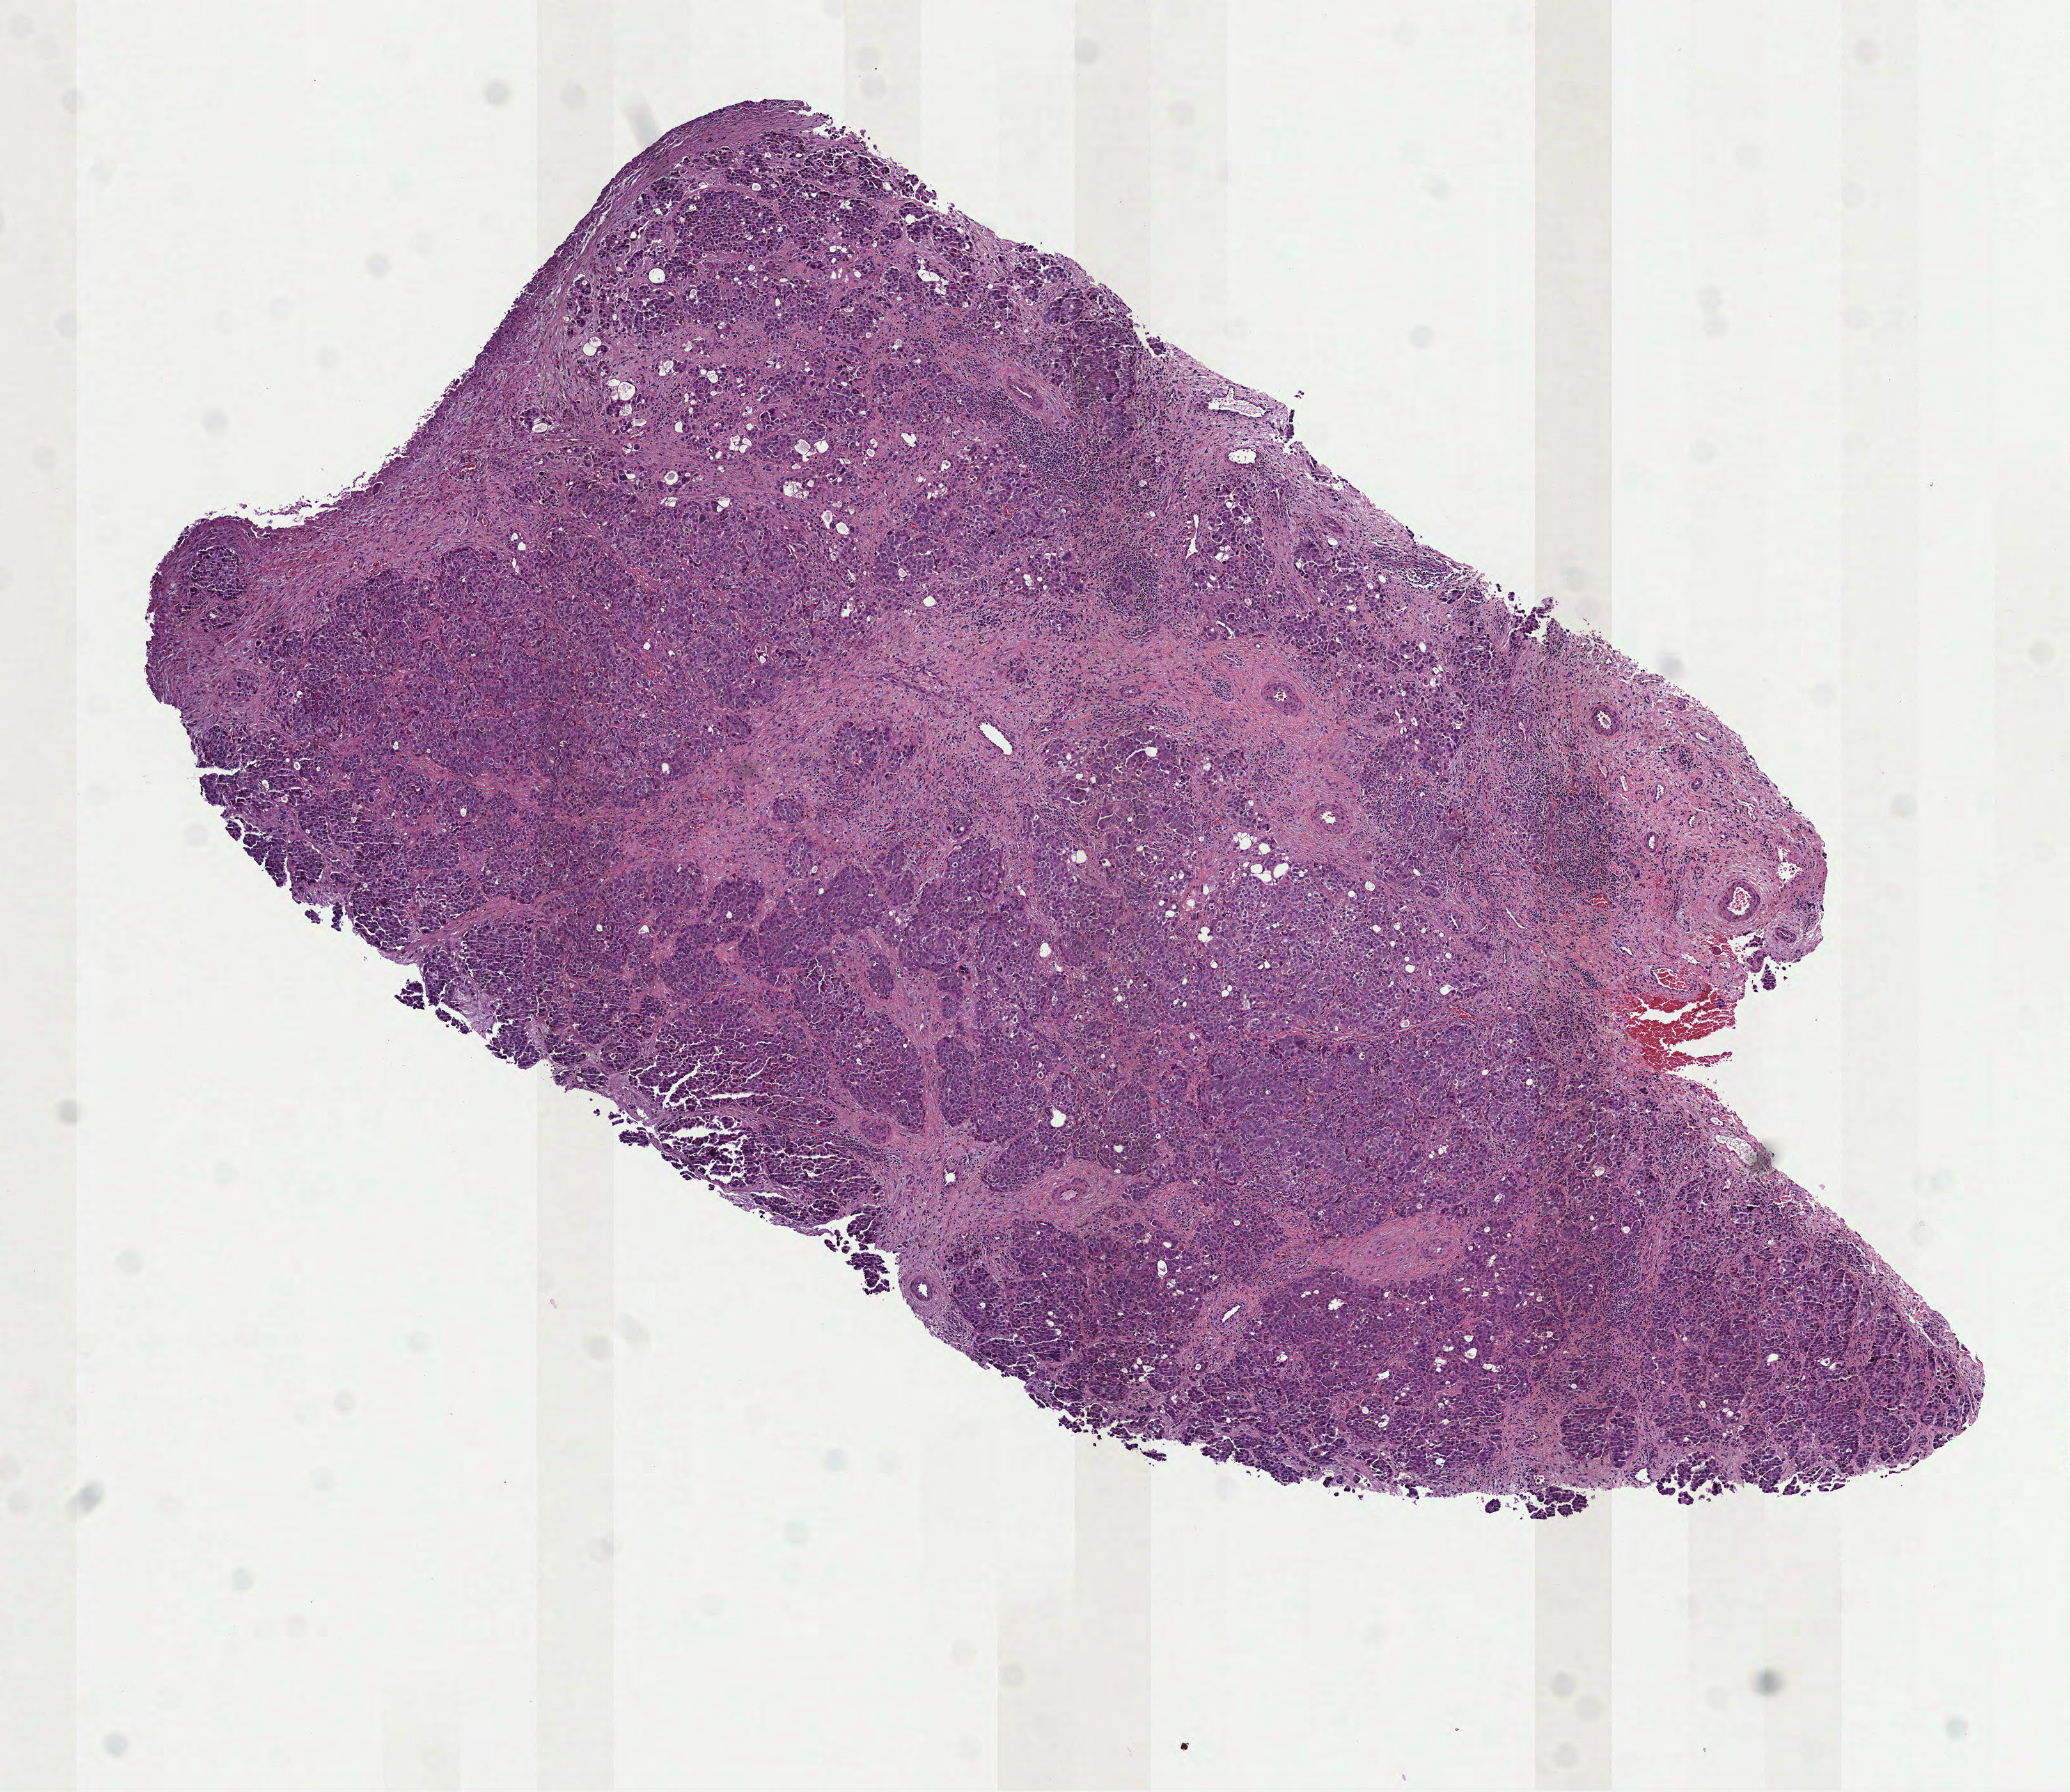
Digitized H&E tissue section (whole slide) — low-resolution overview of the scanned area, about 6.5 x 5.7 mm (slide scanned at 40x), formalin-fixed paraffin-embedded (FFPE) diagnostic section, primary tumour sample from the ovary. Patient: female, age at initial diagnosis 50 years. Histologic grade: G3 (poorly differentiated).
FIGO stage: IIIC. Histologic diagnosis: Serous cystadenocarcinoma, NOS.